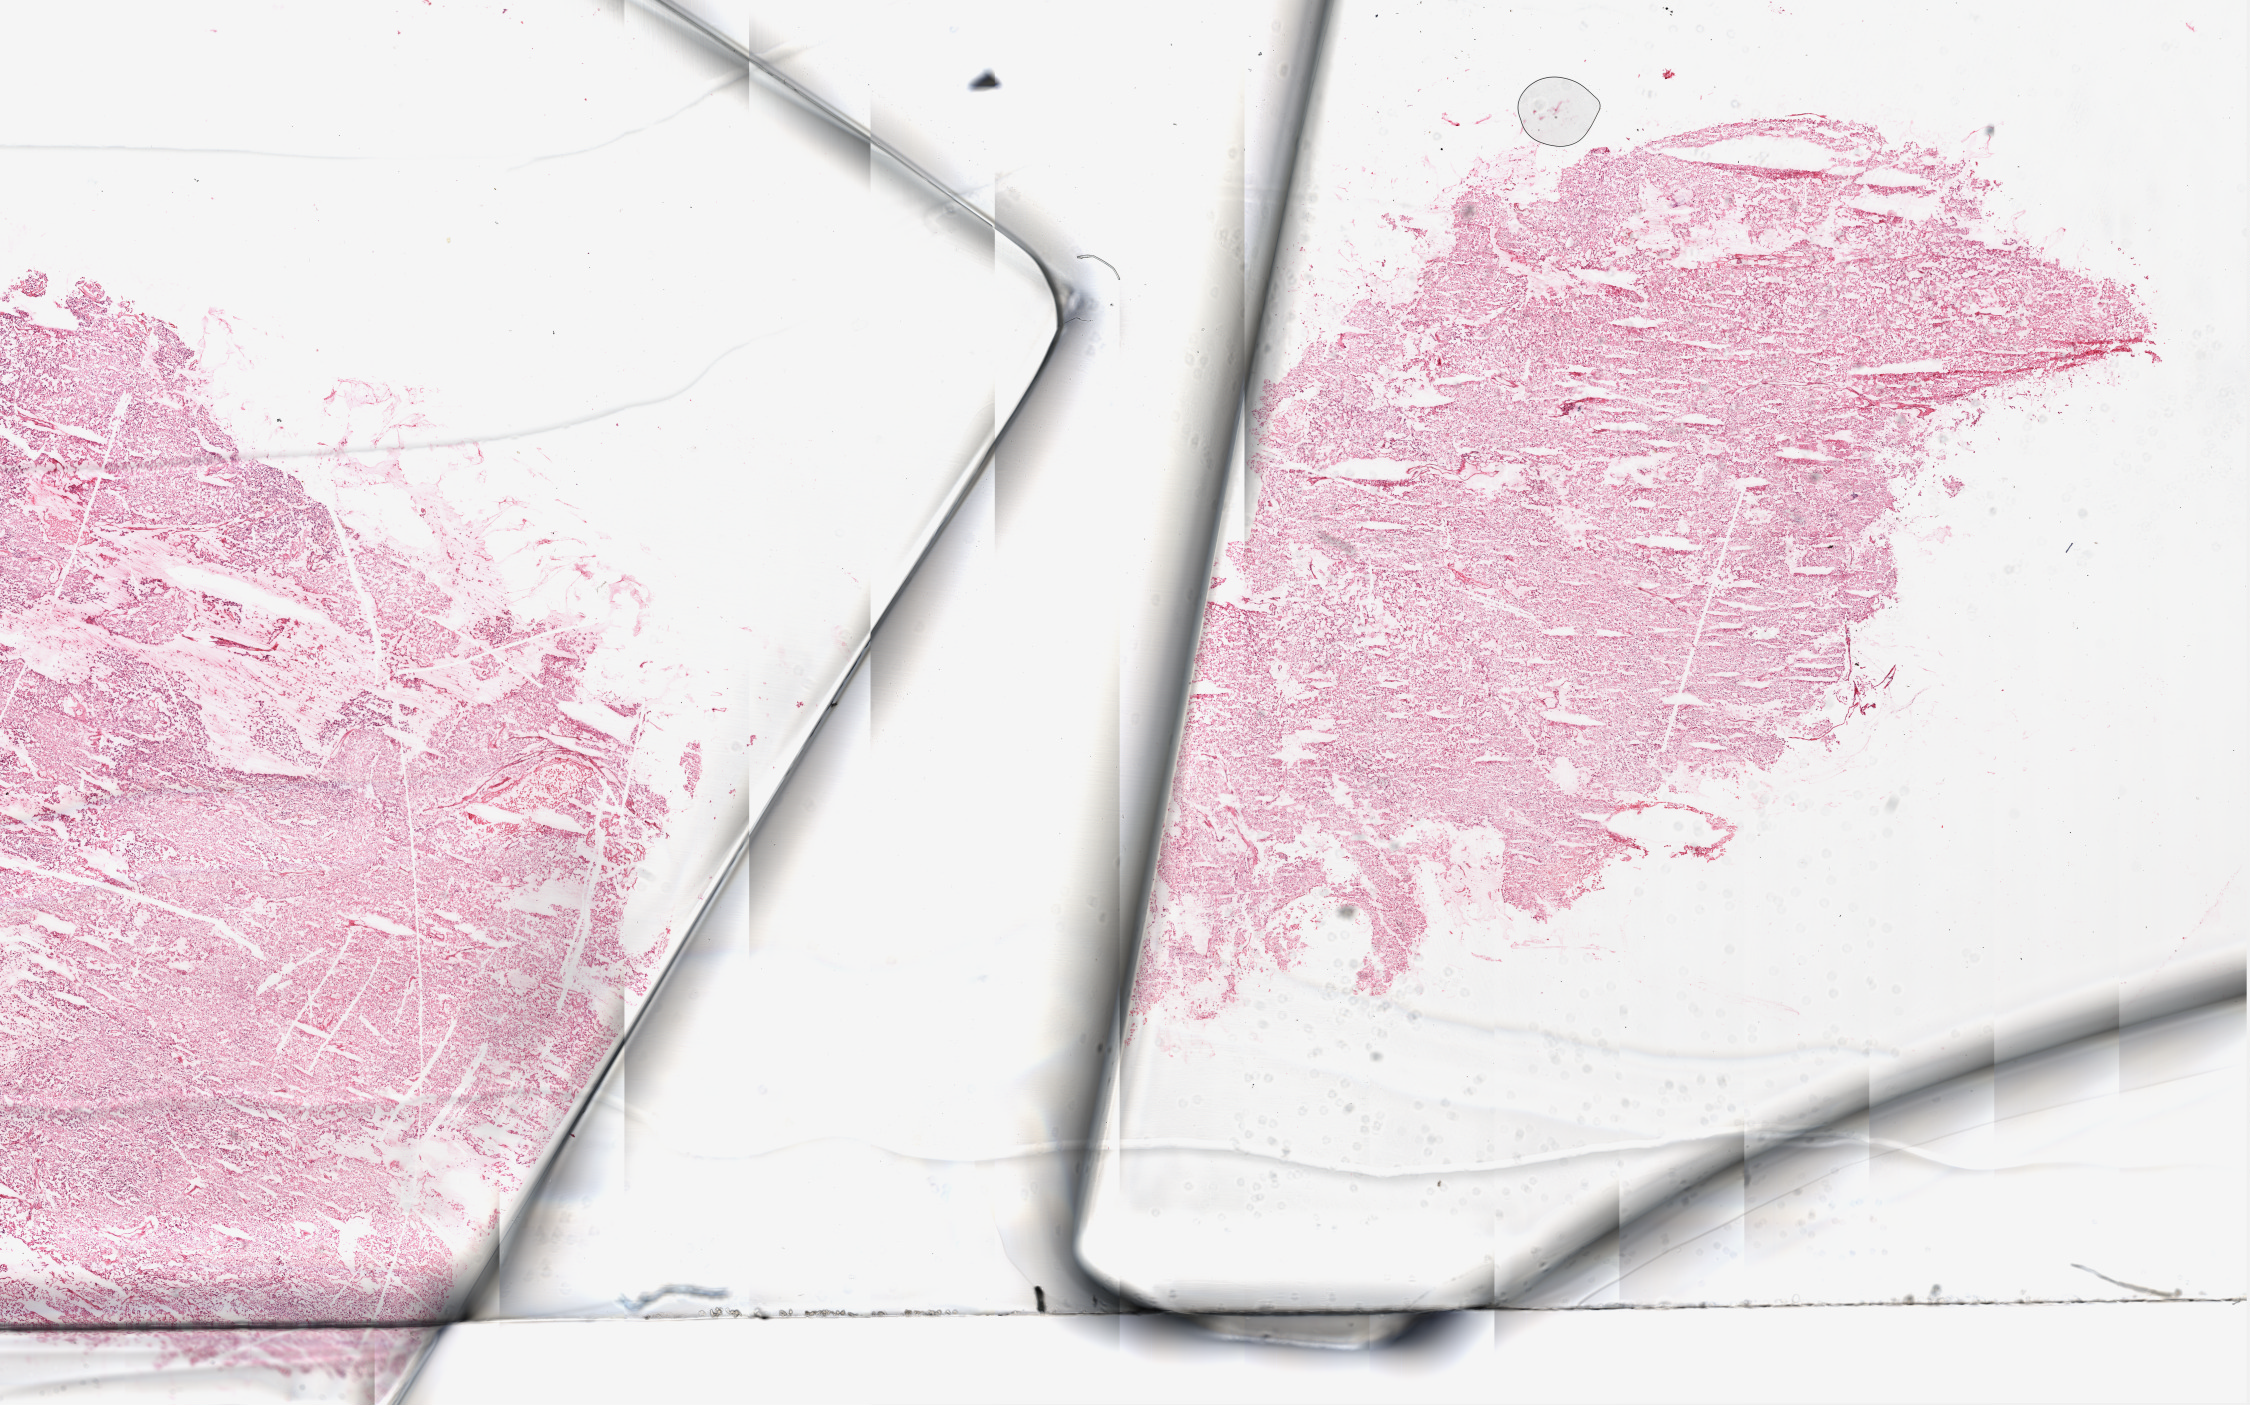
Whole-slide histology image, Hematoxylin and eosin (H&E) stained — whole scanned area (about 18.1 x 11.3 mm, slide scanned at 20x) shown as a low-resolution overview; frozen section; primary tumour sample from the kidney. Male patient; age at initial diagnosis 74 years. Histologic grade: G4 (undifferentiated). Pathologist review of this section (percent, as recorded): tumour cells 95%, tumour nuclei 90%, normal cells 0%, stromal cells 5%, necrosis 0%.
- pathologic diagnosis: Clear cell adenocarcinoma, NOS
- AJCC pathologic stage: IV
- lymph nodes positive (case pathology): 0 of 6 examined